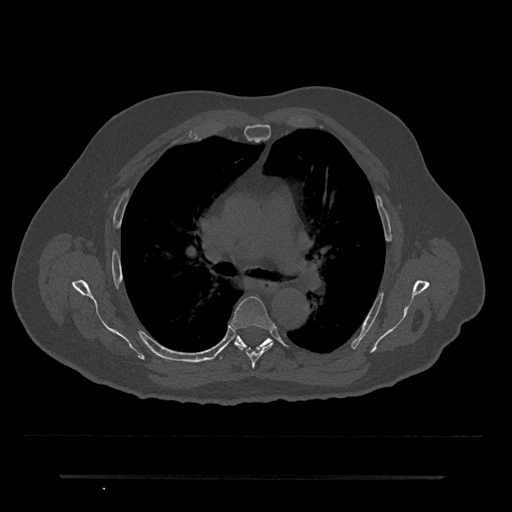
CT including the spine, one axial slice. Slice 465 of 797 in the series (ordered by position). Reconstruction kernel Br40s/3. Bone window (W 1800 / L 400 HU). 512 × 512 image matrix. Male patient, age 69 years. From the clinical record (not read from this slice): primary cancer: prostate.
Outlined on this slice (semi-automatic segmentation, software-assisted and operator-edited):
- T5 vertebra: bounding box [x1, y1, x2, y2] px = [231, 296, 274, 368]
- T6 vertebra: [219, 336, 271, 360]